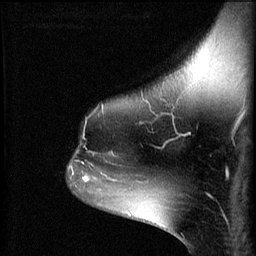
Breast MRI (dynamic contrast-enhanced), one sagittal slice; position 46 of 60 along the scan axis; 3 images stored at this slice position (order not interpretable as contrast timing); 1.5 T; TE 4.2 ms, TR 8.2 ms; 2 mm slice thickness; 256 × 256 image matrix, field of view 180 × 180 mm. Patient: female, 49 years.
Structures marked on this image (semi-automatically segmented with operator editing):
- analysis volume of interest (the breast-tissue region the enhancement analysis was run in; not a lesion): bounding box (x1, y1, x2, y2) in pixels: (69, 142, 109, 187)
- tumour enhancement mask (voxels above the 70 % enhancement threshold inside the analysis volume of interest): (69, 168, 107, 183)